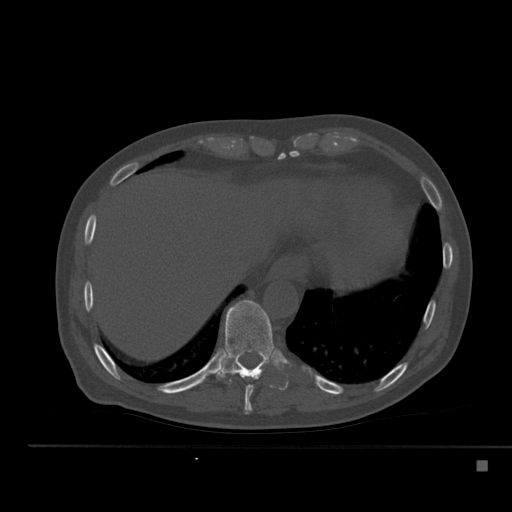
CT including the spine, one axial slice; position 273 of 517 along the scan axis; reconstruction kernel Br40s; 120 kVp; bone window (W 1800 / L 400 HU); 1.5 mm slice thickness; 512 × 512 image matrix, field of view 408 × 408 mm. Male patient, age 70 years. From the clinical record (not read from this slice): primary cancer: renal.
Outlined on this slice (semi-automatically segmented with operator editing):
- T10 vertebra: bounding box <218,300,274,384> (left, top, right, bottom; pixels)
- T9 vertebra: <244,378,257,414>